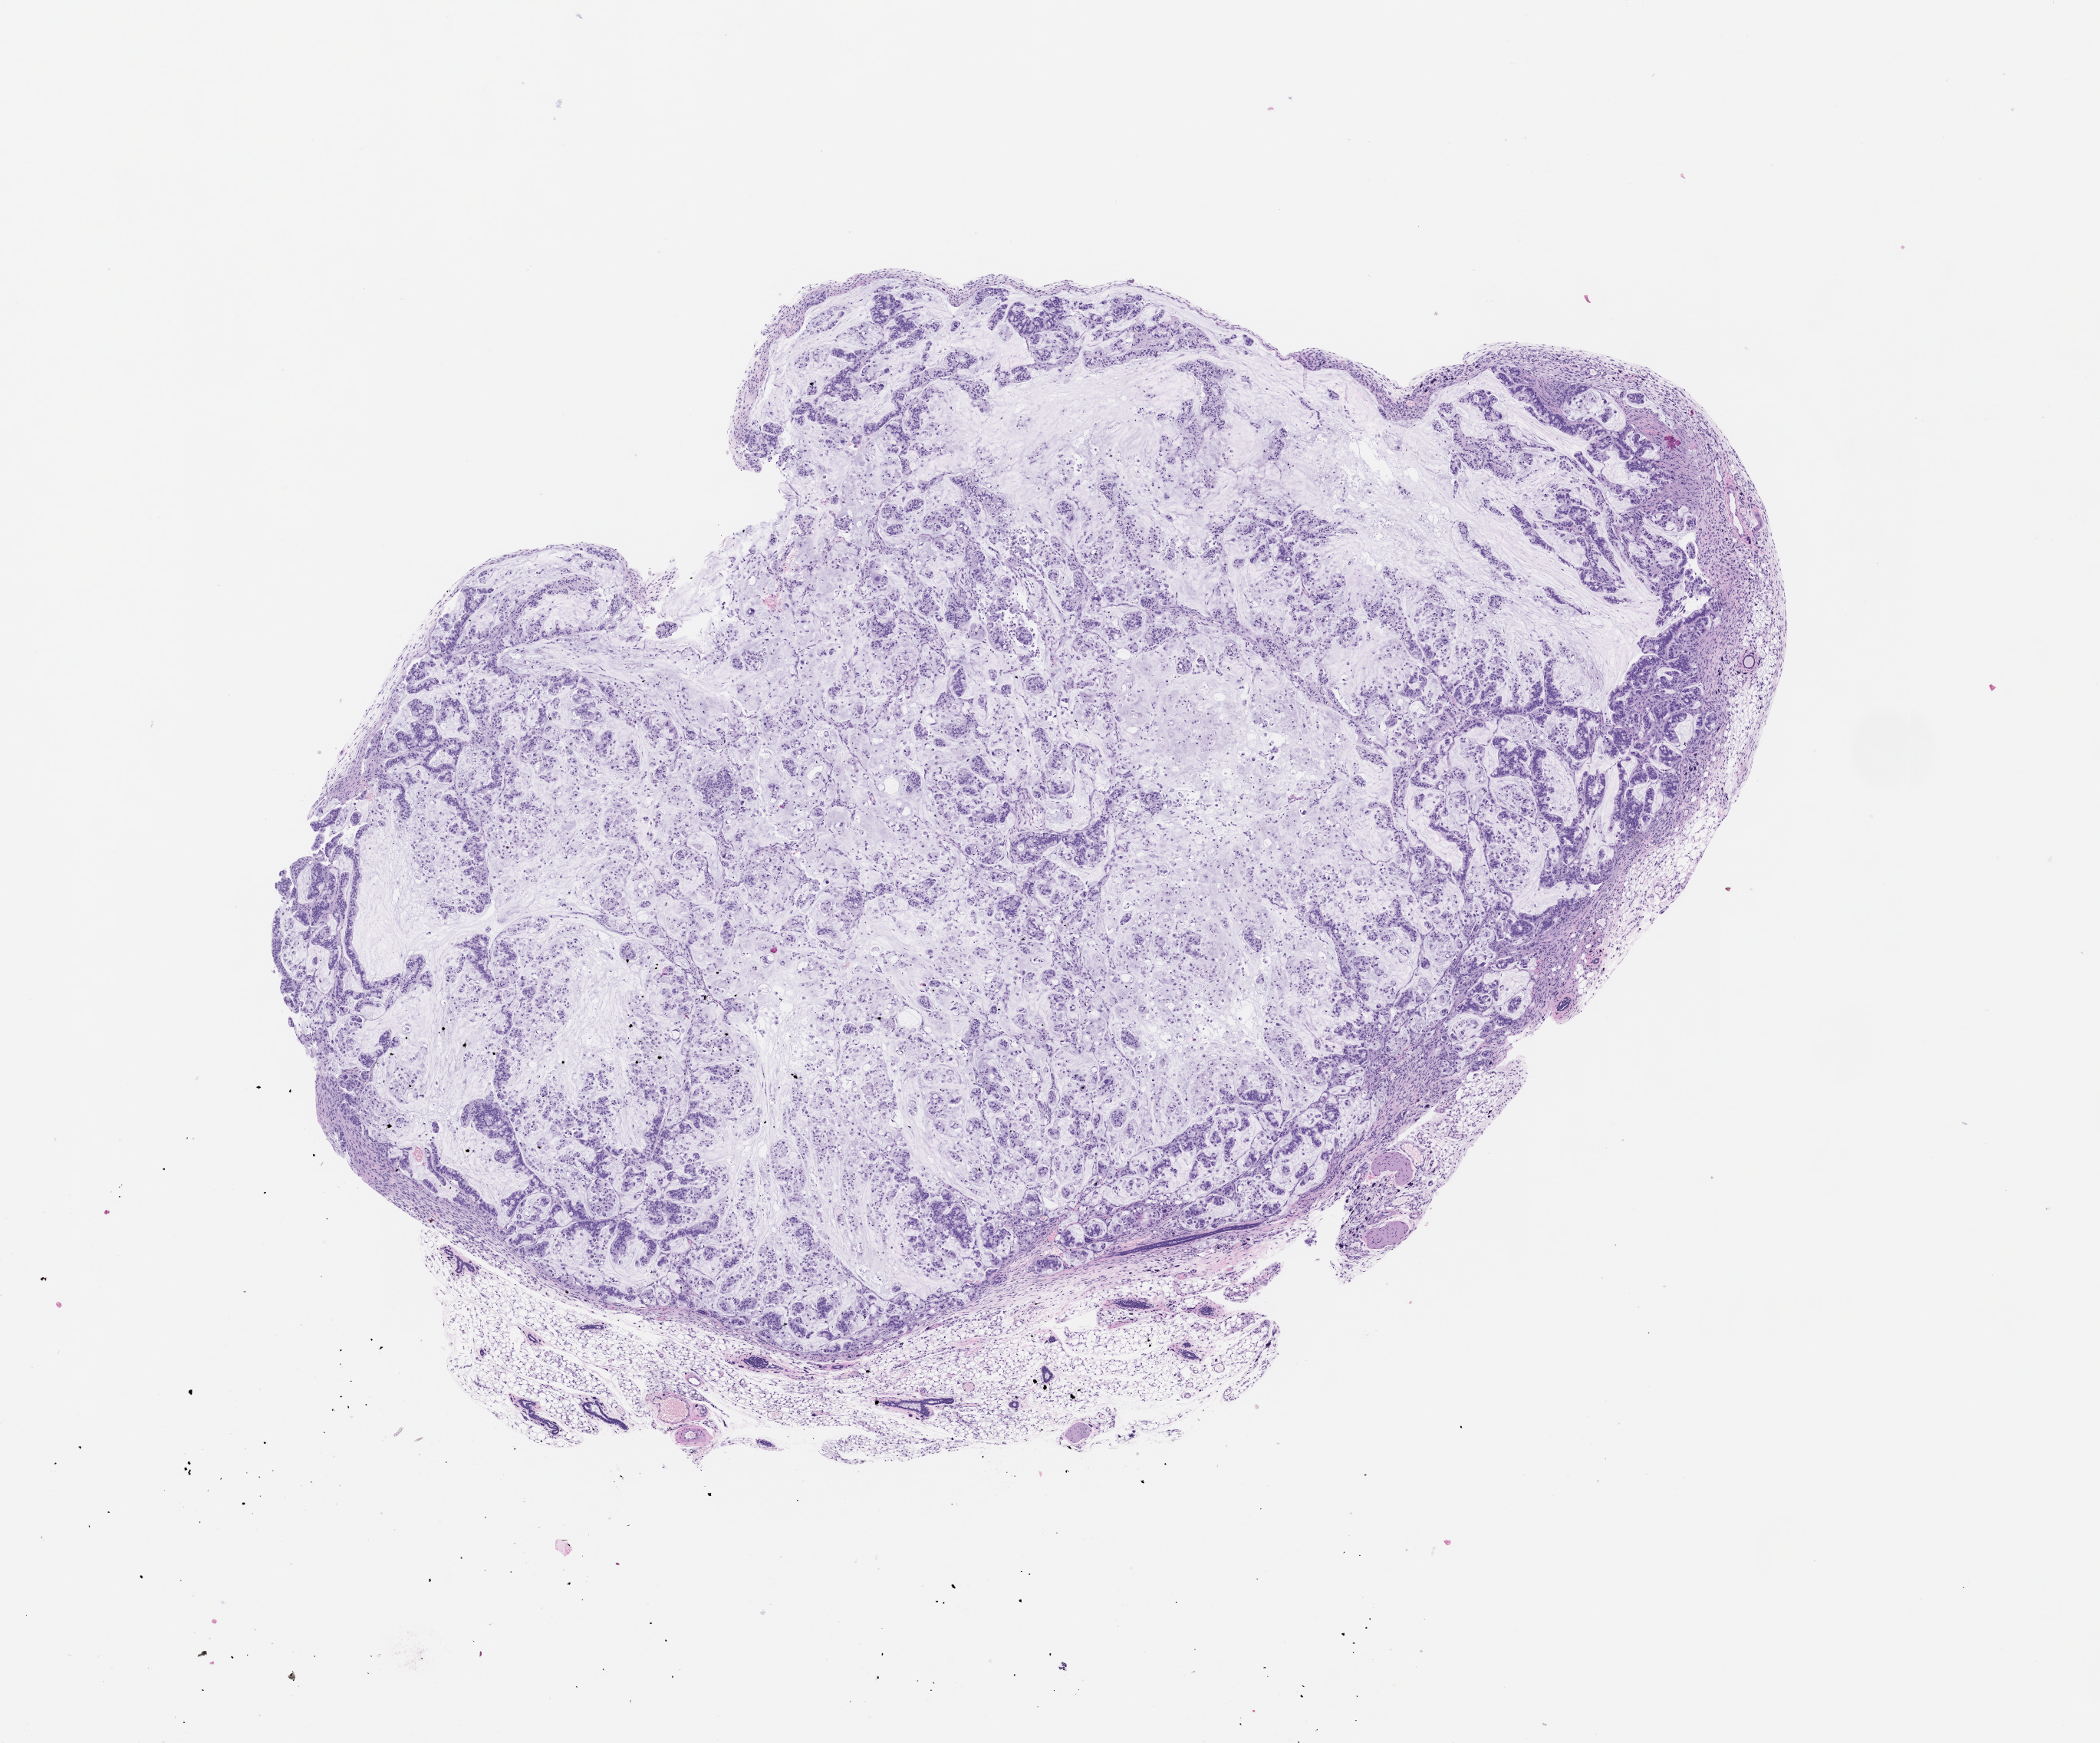
H&E whole-slide image of a patient-derived xenograft (PDX) tumor grown in a mouse, passage 1, whole scanned area (about 11.0 x 9.1 mm) shown as a low-resolution overview; FFPE section; tumor site category: pancreas.
Originating patient diagnosis: Pancreatic Adenocarcinoma.